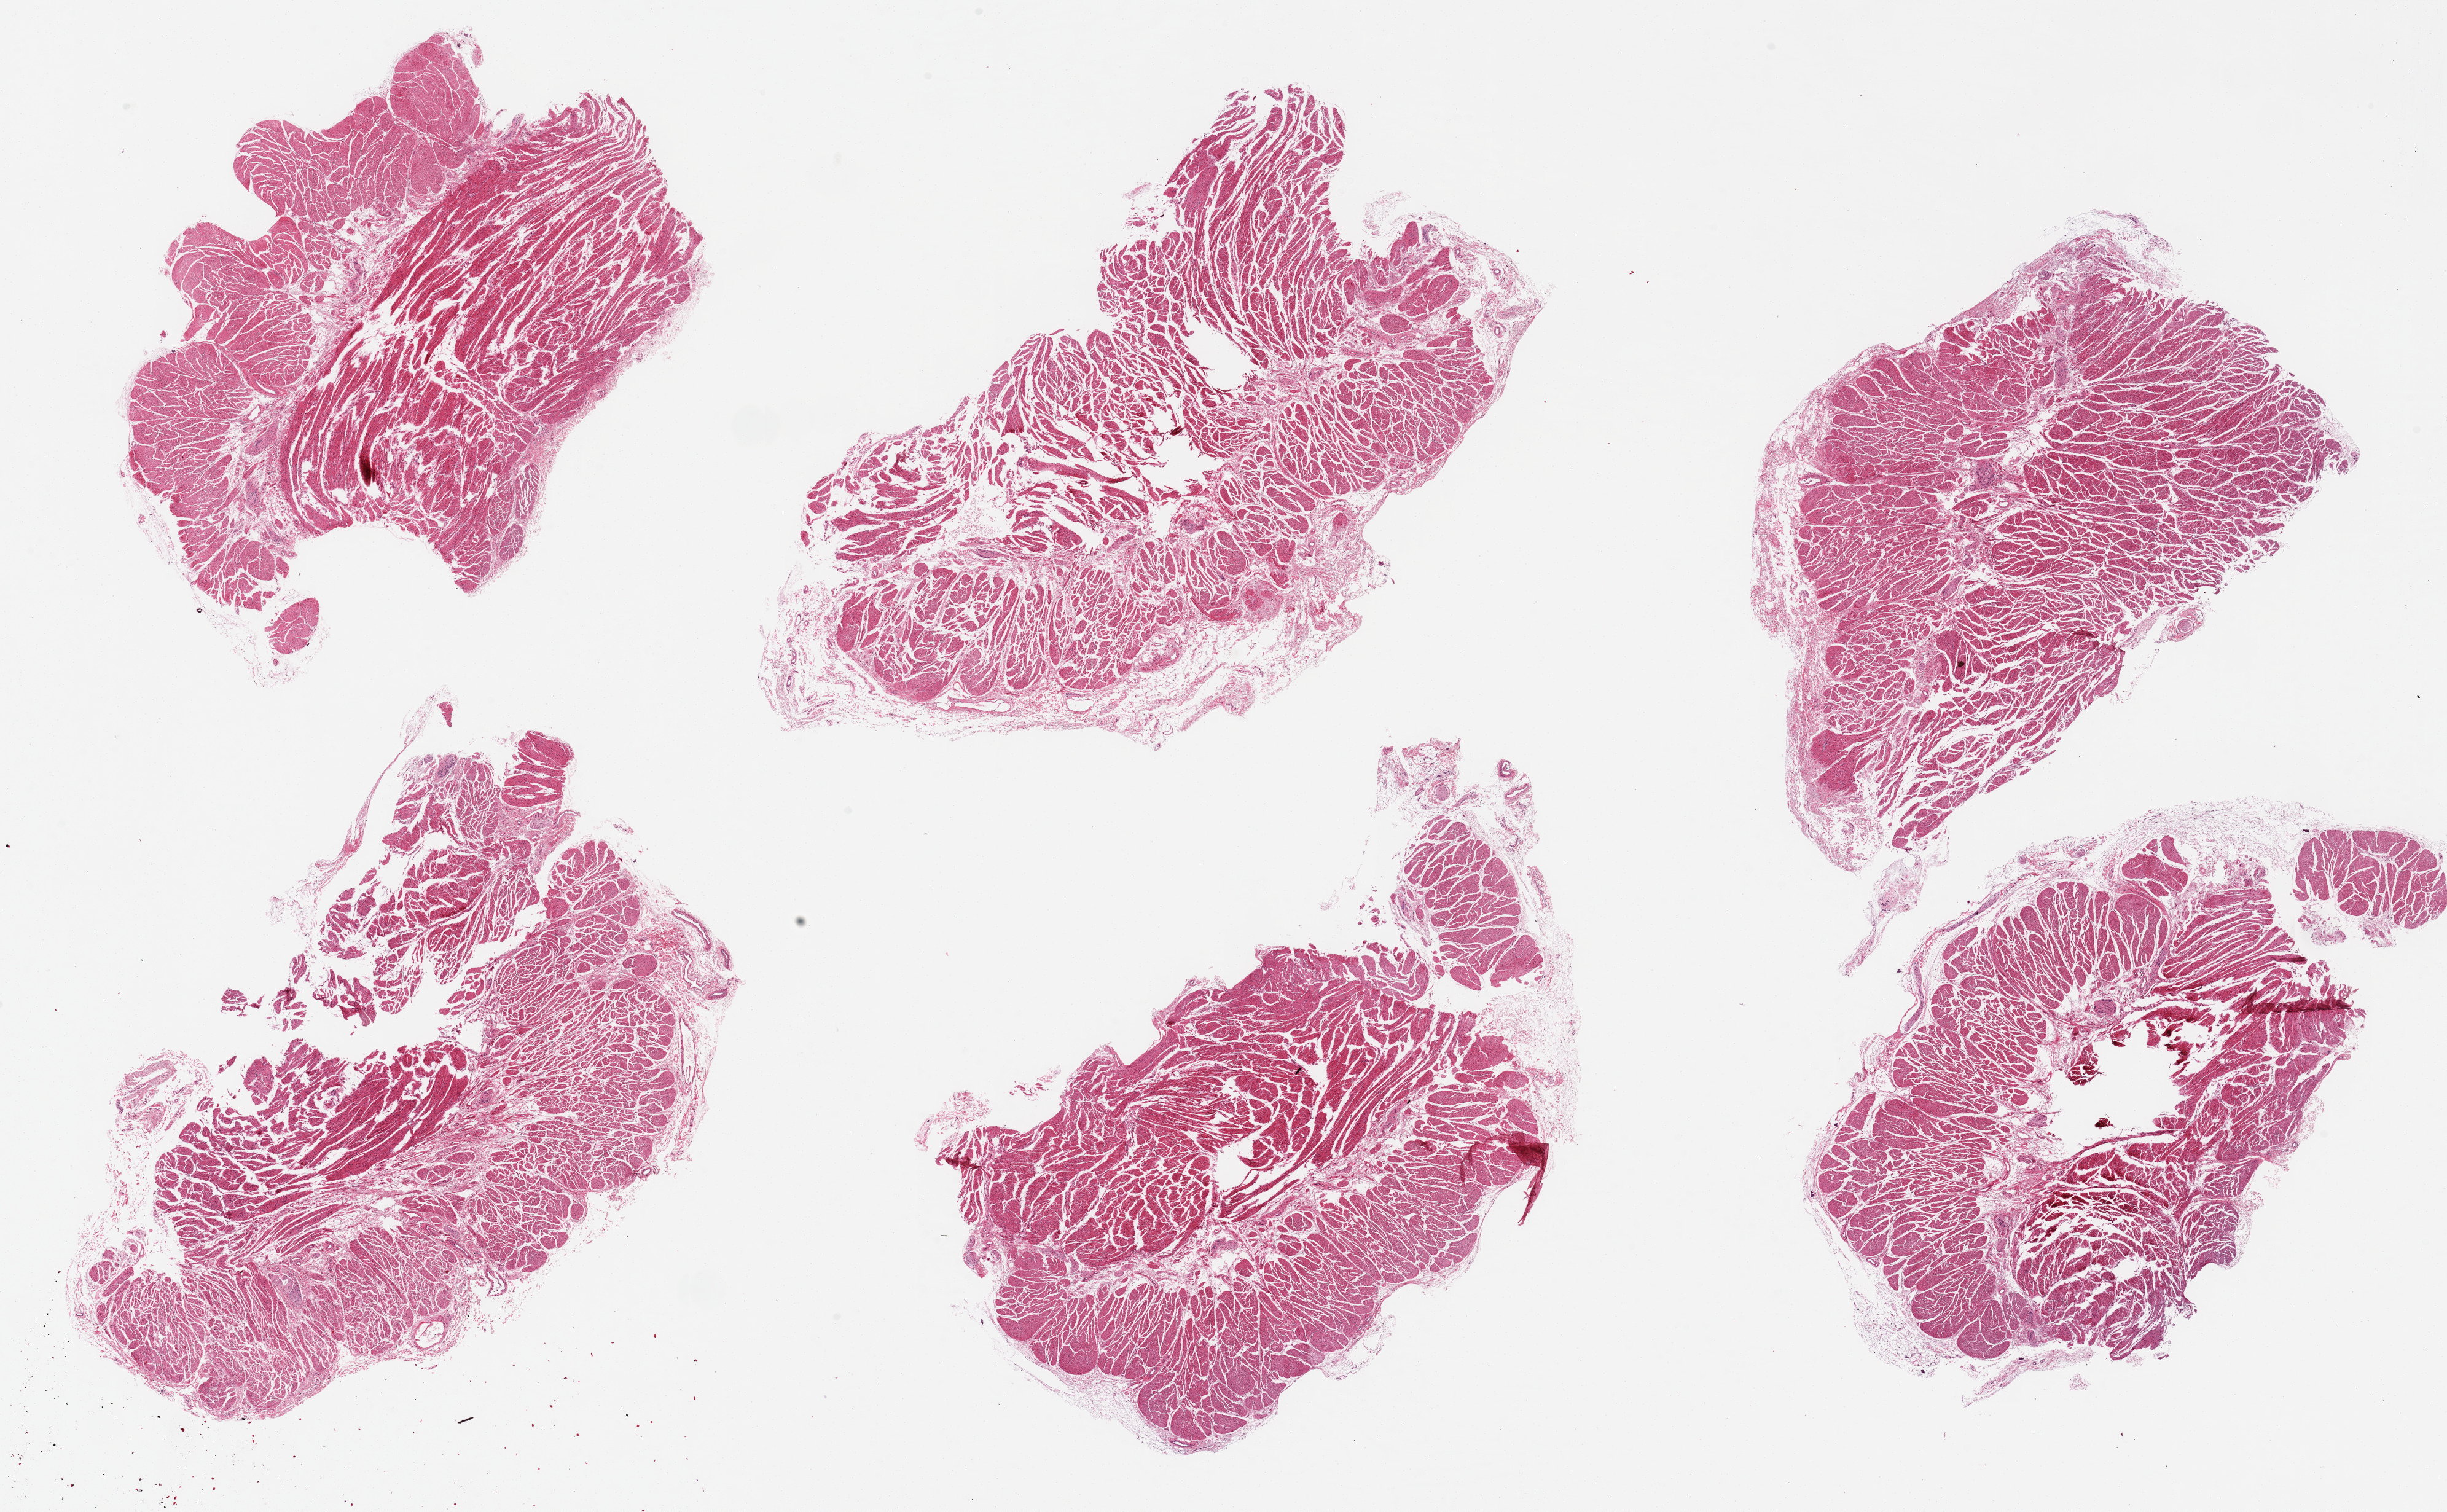
Hematoxylin and eosin (H&E) whole-slide image, brightfield, low-resolution overview of the scanned area, about 31.5 x 19.5 mm (slide scanned at 20x), PAXgene-fixed, paraffin-embedded tissue, target tissue: esophageal muscle, tissue donor sample. Donor sex: male.
Pathologist's review note for this sample: 6 pieces up to 9x5 mm.